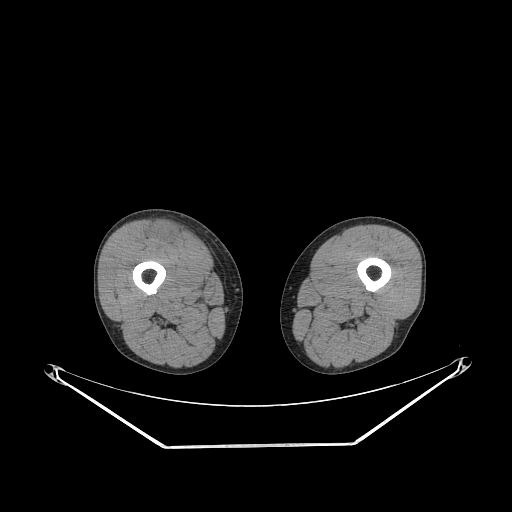
CT of an extremity soft-tissue mass (from a PET/CT study), one axial slice; slice 238 of 311 in the series (ordered by position); reconstruction kernel STANDARD; soft-tissue window (W 400 / L 40 HU); 3.75 mm slice thickness; 512 × 512 image matrix, field of view 500 × 500 mm. Male patient. Case-level facts recorded for this patient, not image findings: histological type: pleiomorphic leiomyosarcoma; grade: intermediate; site of the primary tumour: right thigh.
Outlined on this slice (expert contour drawn on MRI and transferred to this co-registered scan by the dataset authors):
- gross tumour volume including surrounding oedema: box from (x=153, y=224) to (x=181, y=243) px